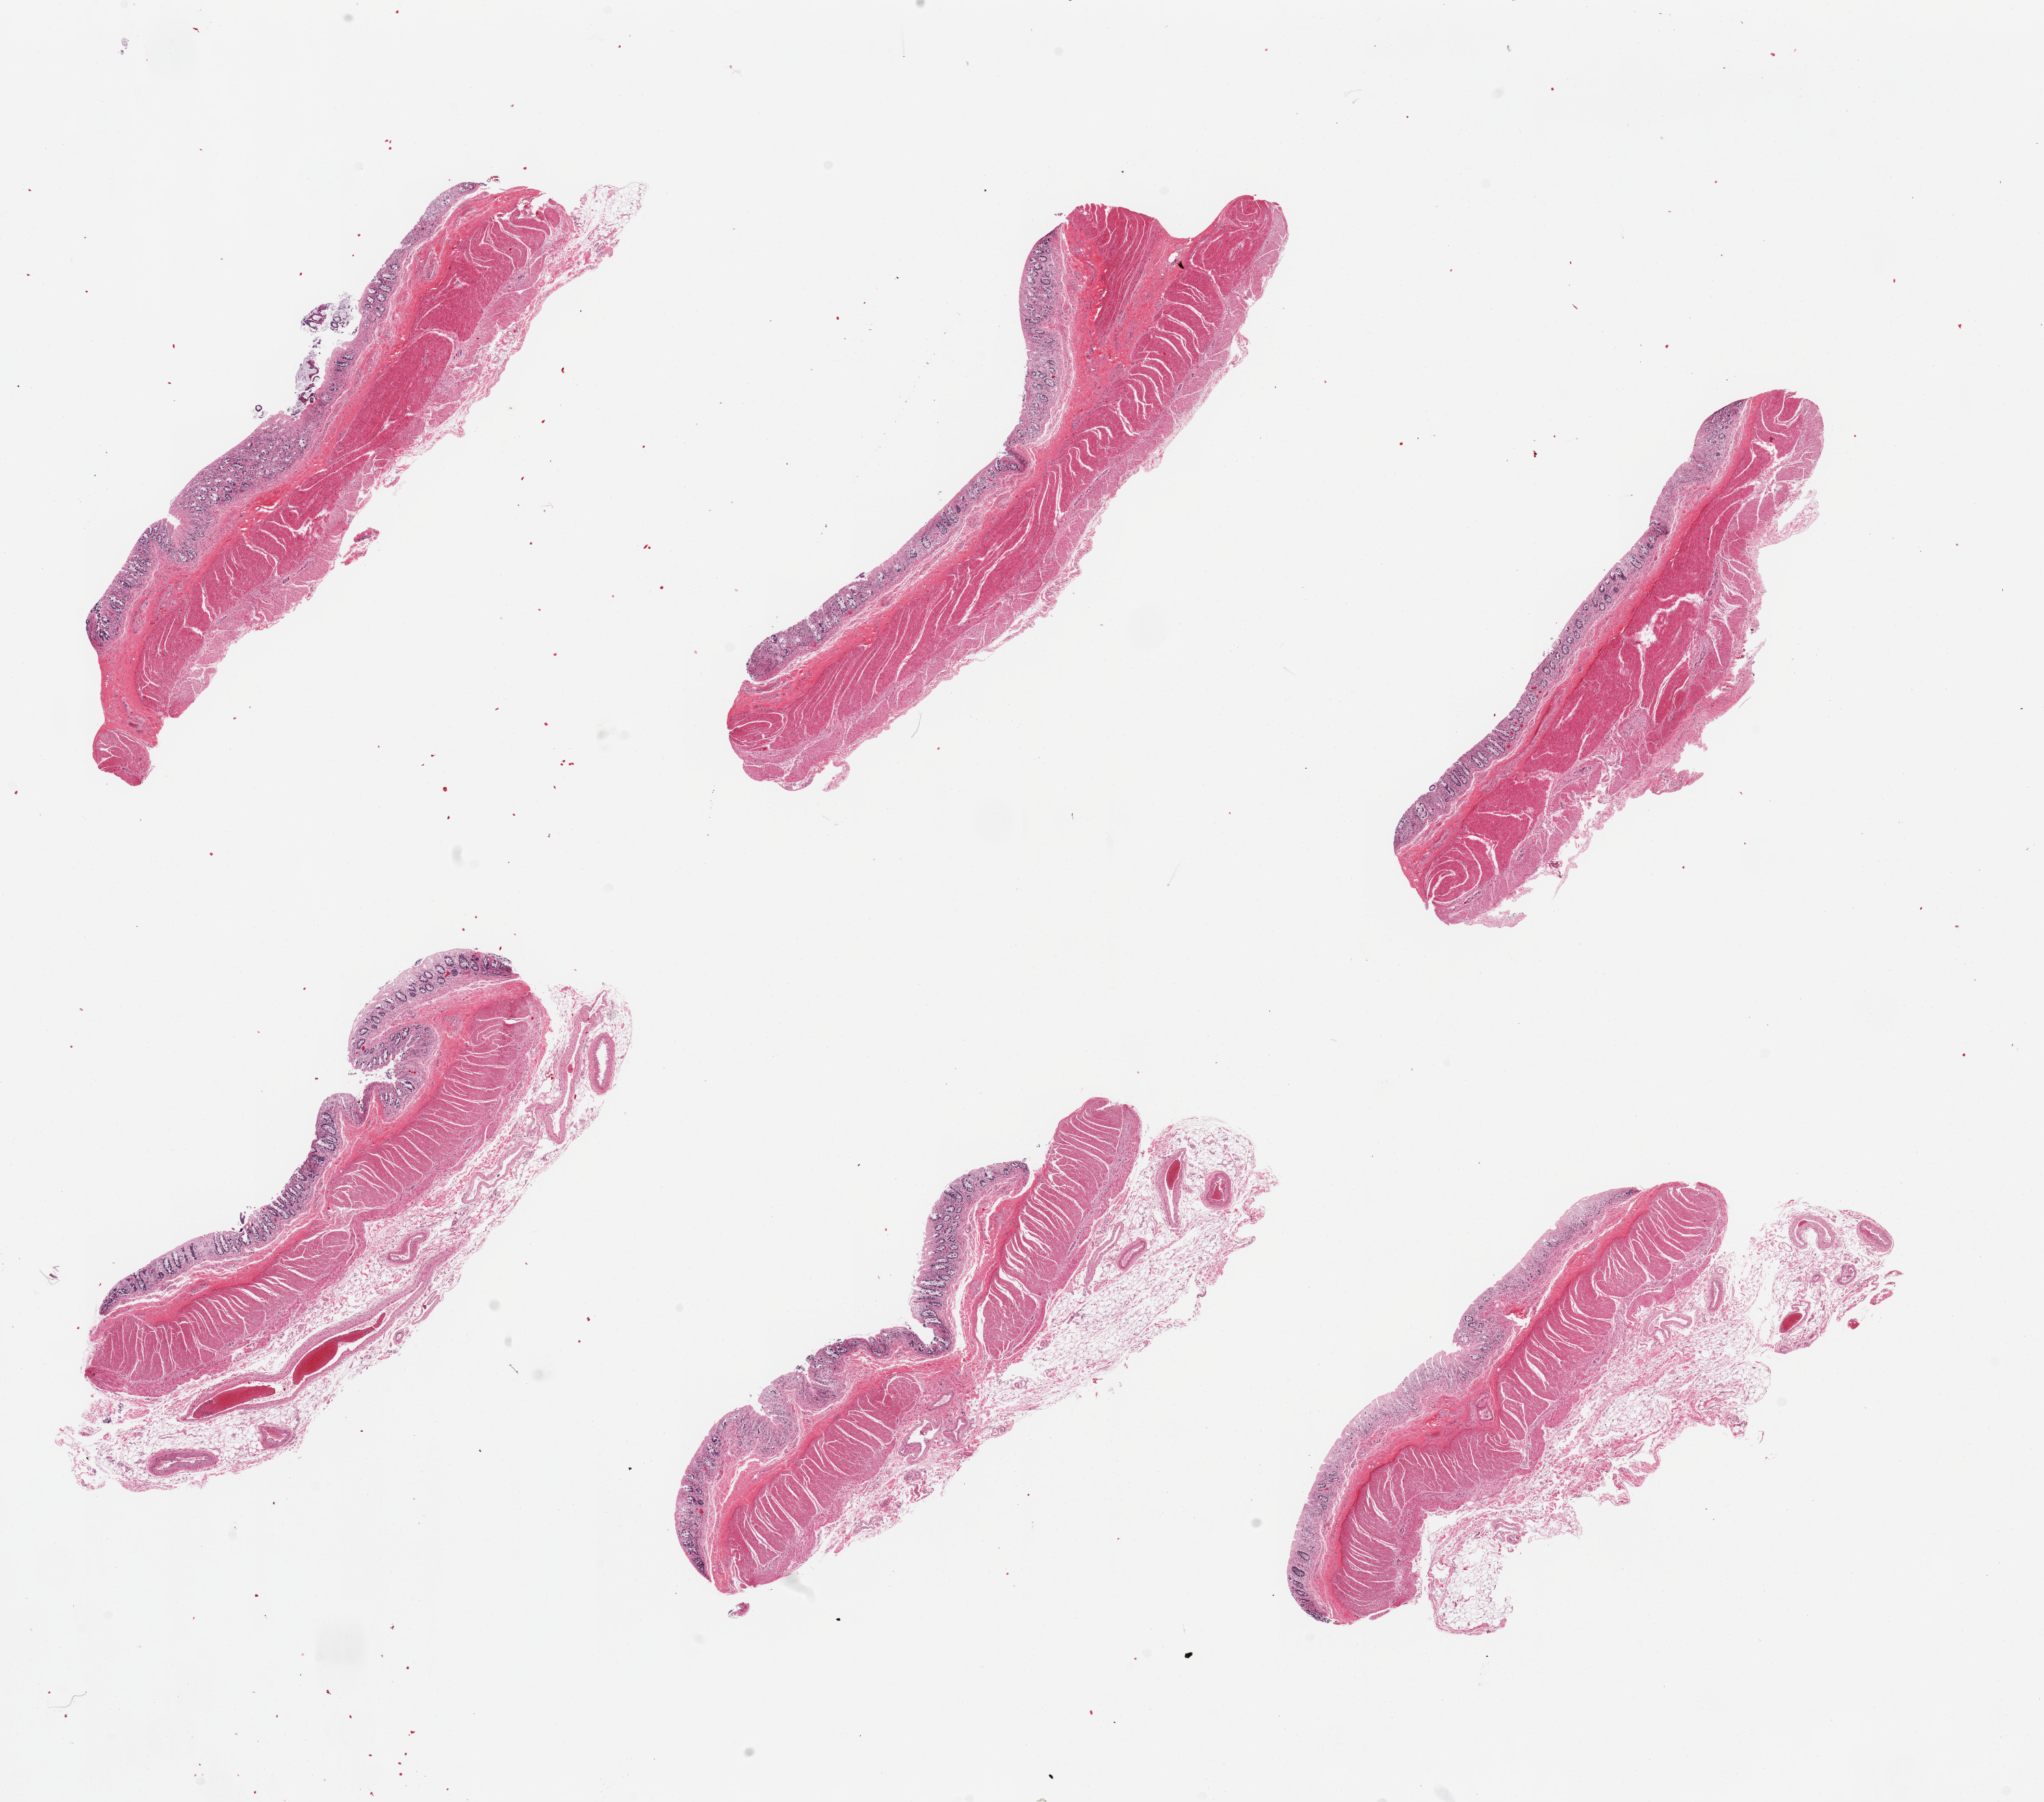
H&E whole-slide image, brightfield — shown as a low-resolution overview of the whole scanned area (about 23.6 x 20.8 mm). PAXgene-fixed paraffin-embedded (PFPE) section. Section of transverse colon (target tissue). Tissue donor sample. Female donor.
Review note (as recorded): 6 pieces, mucosa is ~20-30% thickness but totally autolyzed/sloughed.